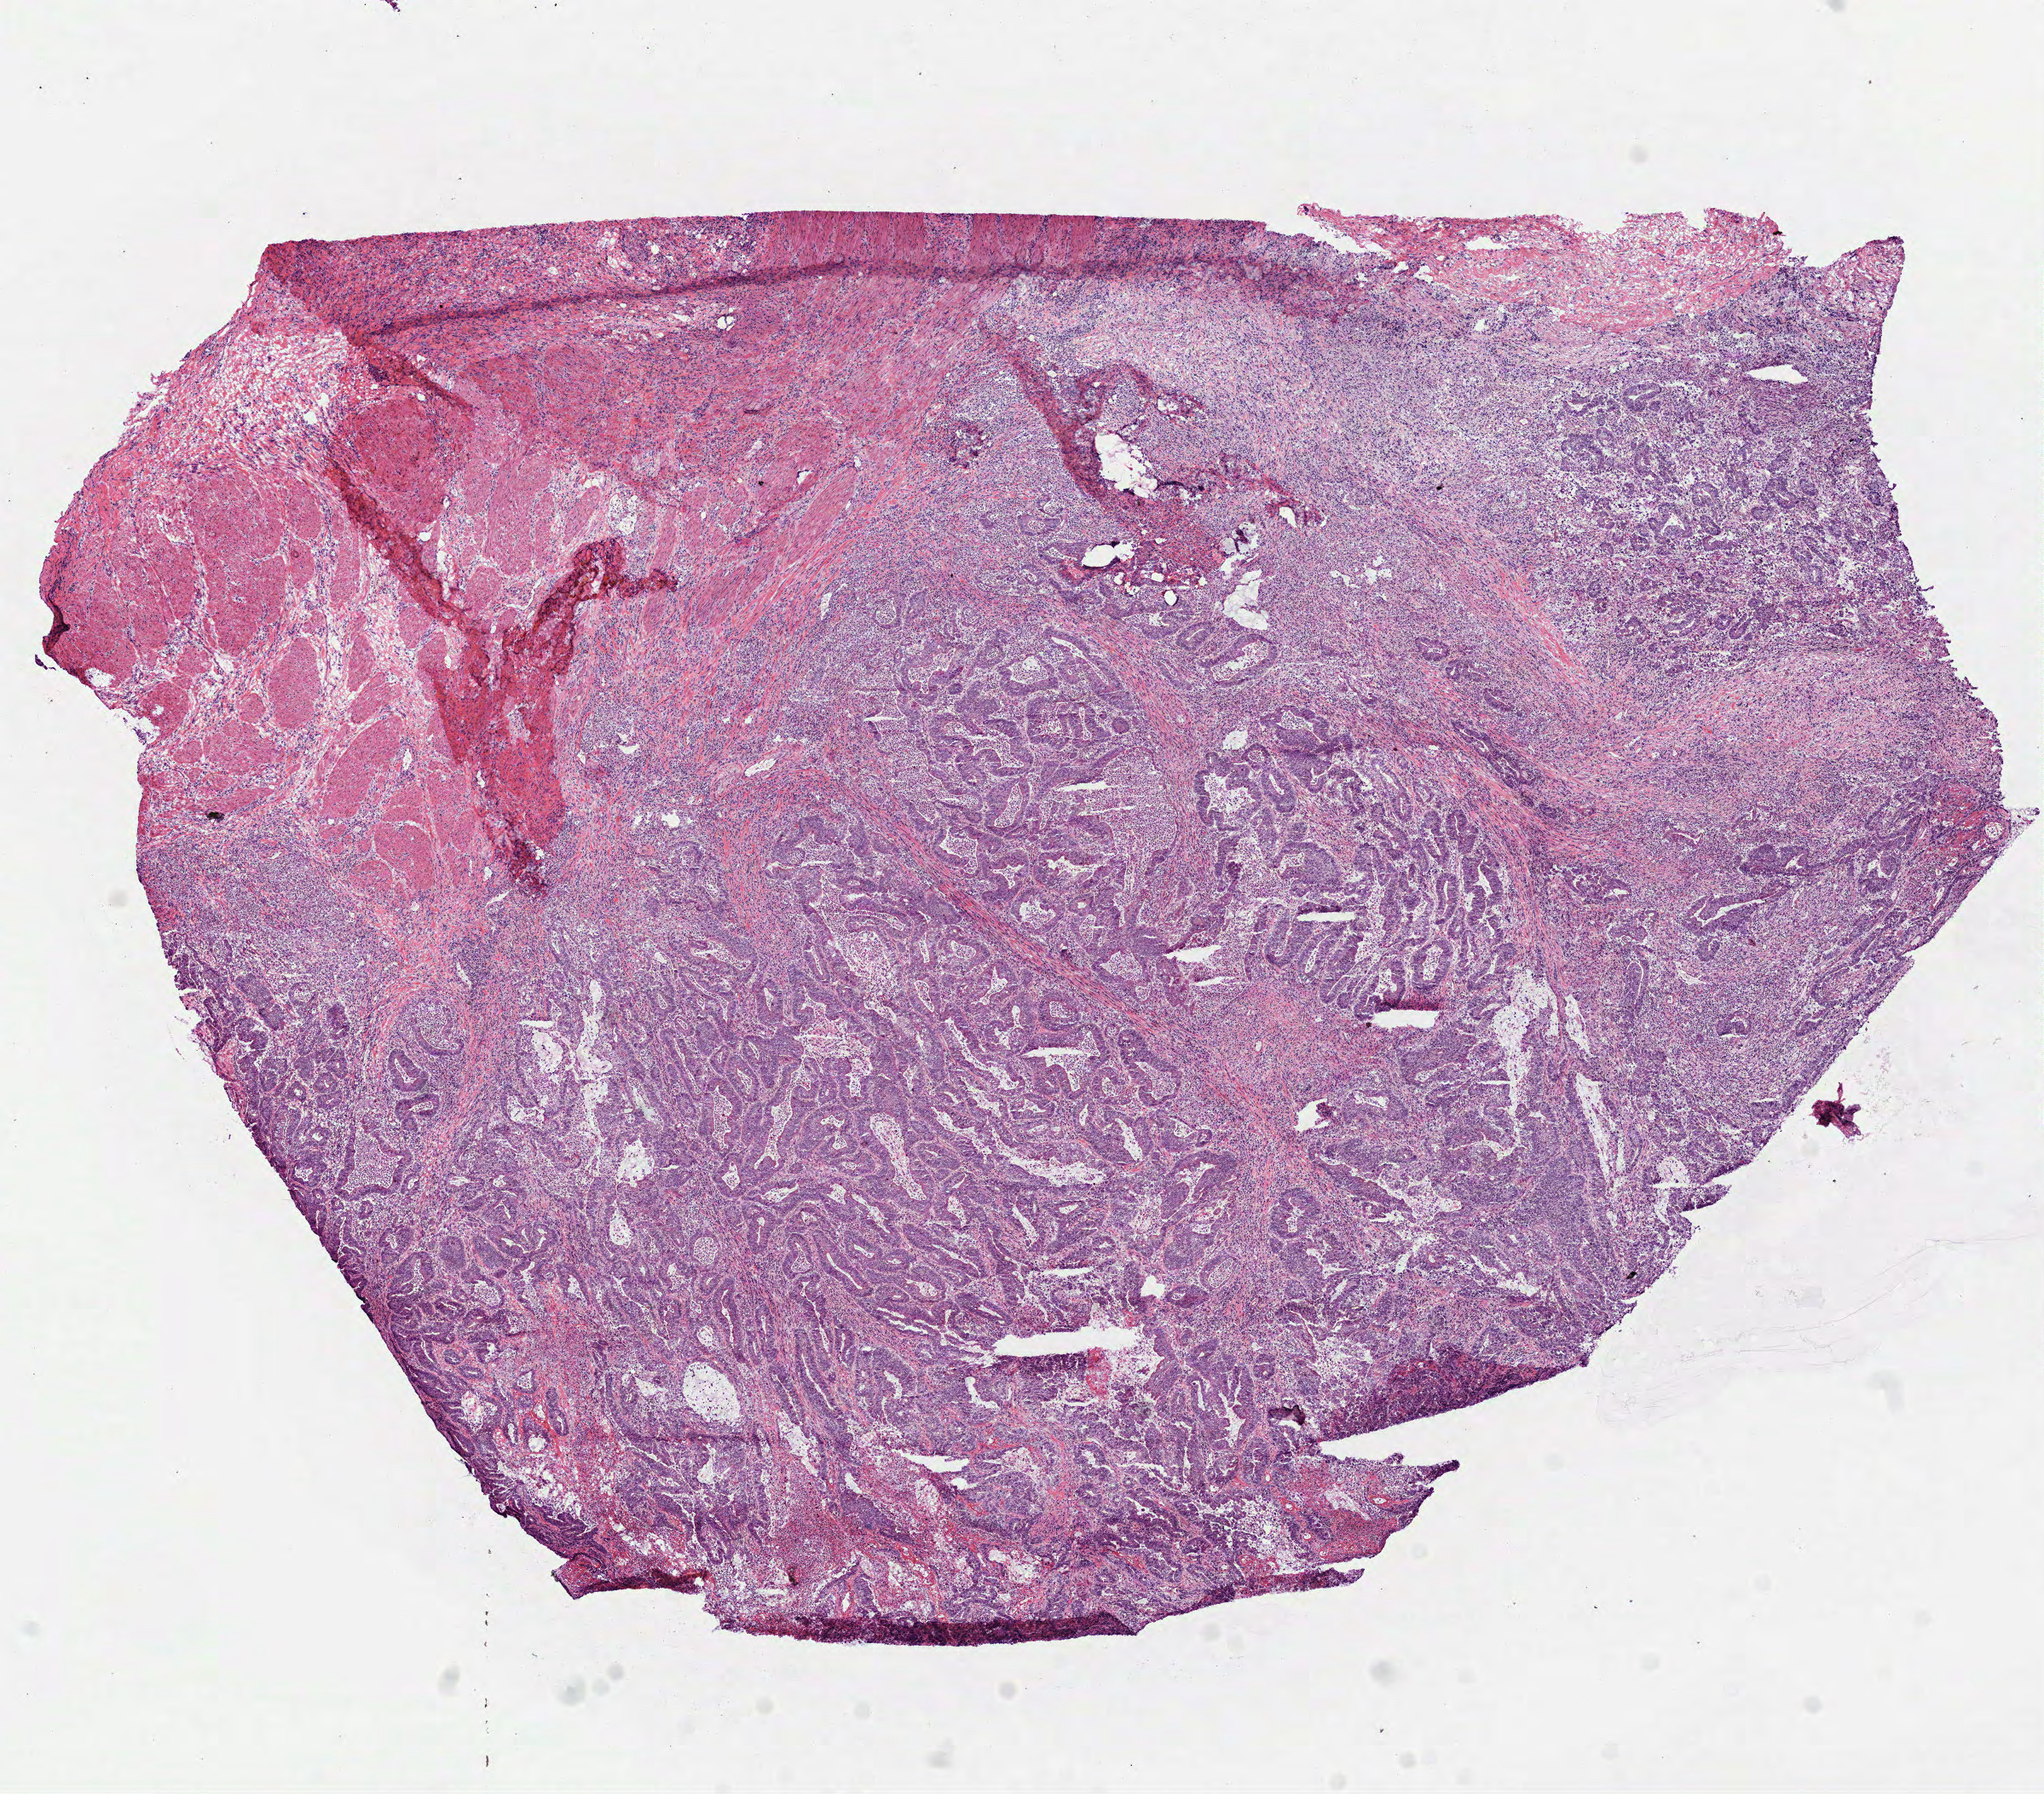
Digitized H&E tissue section (whole slide) — low-resolution overview of the scanned area, about 9.7 x 8.5 mm (from a 40x scan), frozen section, primary tumour sample from the rectum. Male, age 73 years at initial diagnosis.
Diagnosis: Adenocarcinoma, NOS.